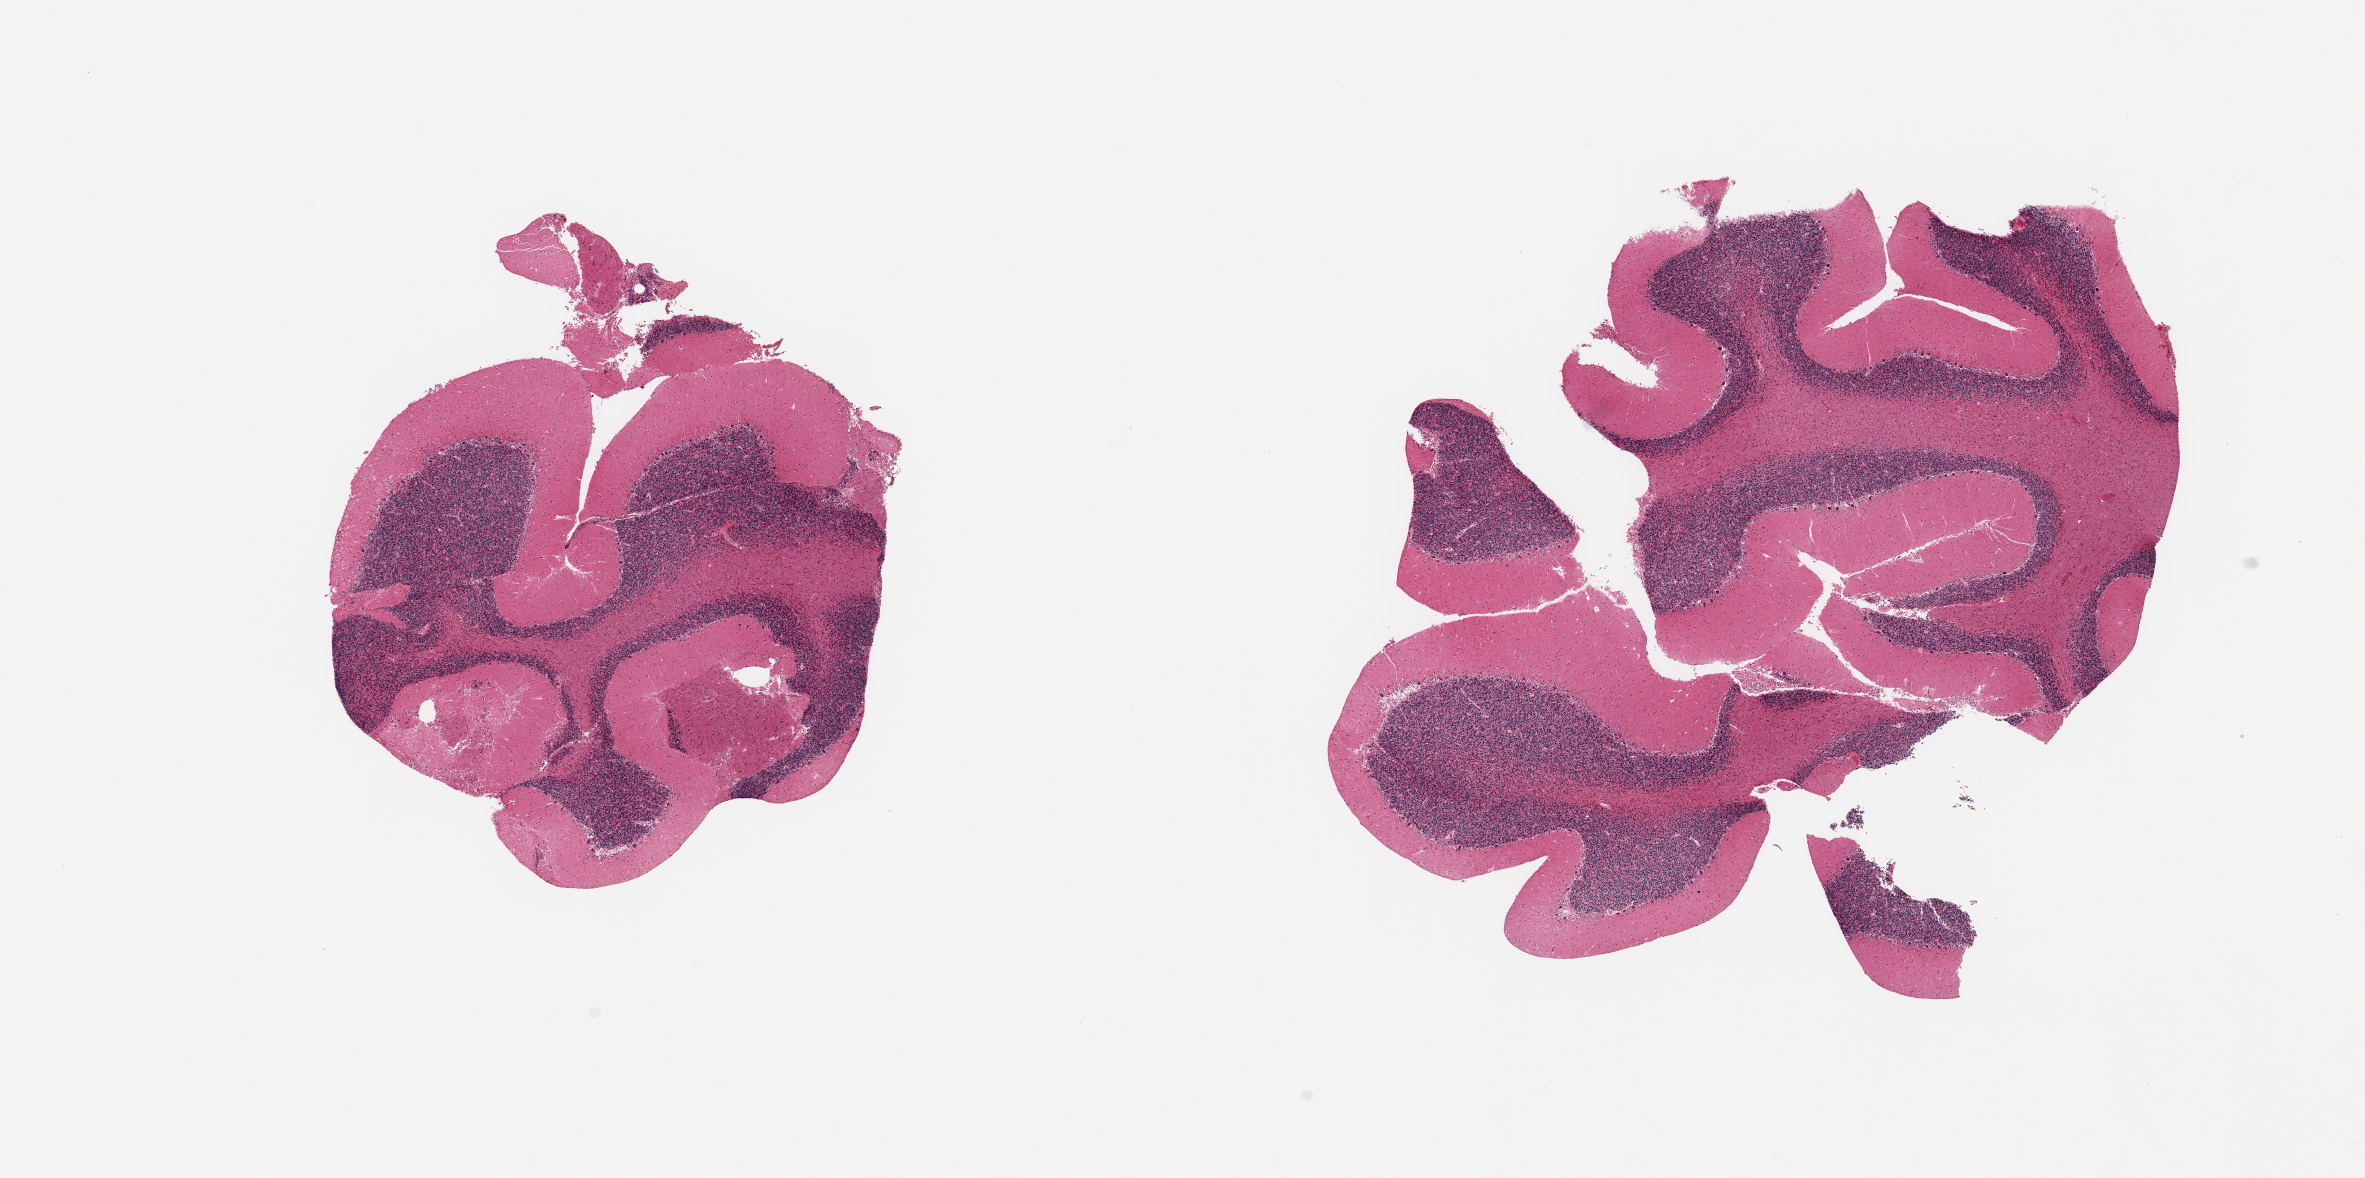
Whole-slide image, H&E stain, shown as a low-resolution overview of the whole scanned area (about 18.7 x 9.3 mm, slide scanned at 20x). PAXgene-fixed paraffin-embedded (PFPE) section. Sampled site (target tissue): cerebellum. Donor tissue sample. Donor sex: male.
Pathologist's review note for this sample: 2 pieces; Purkinje cells observed.